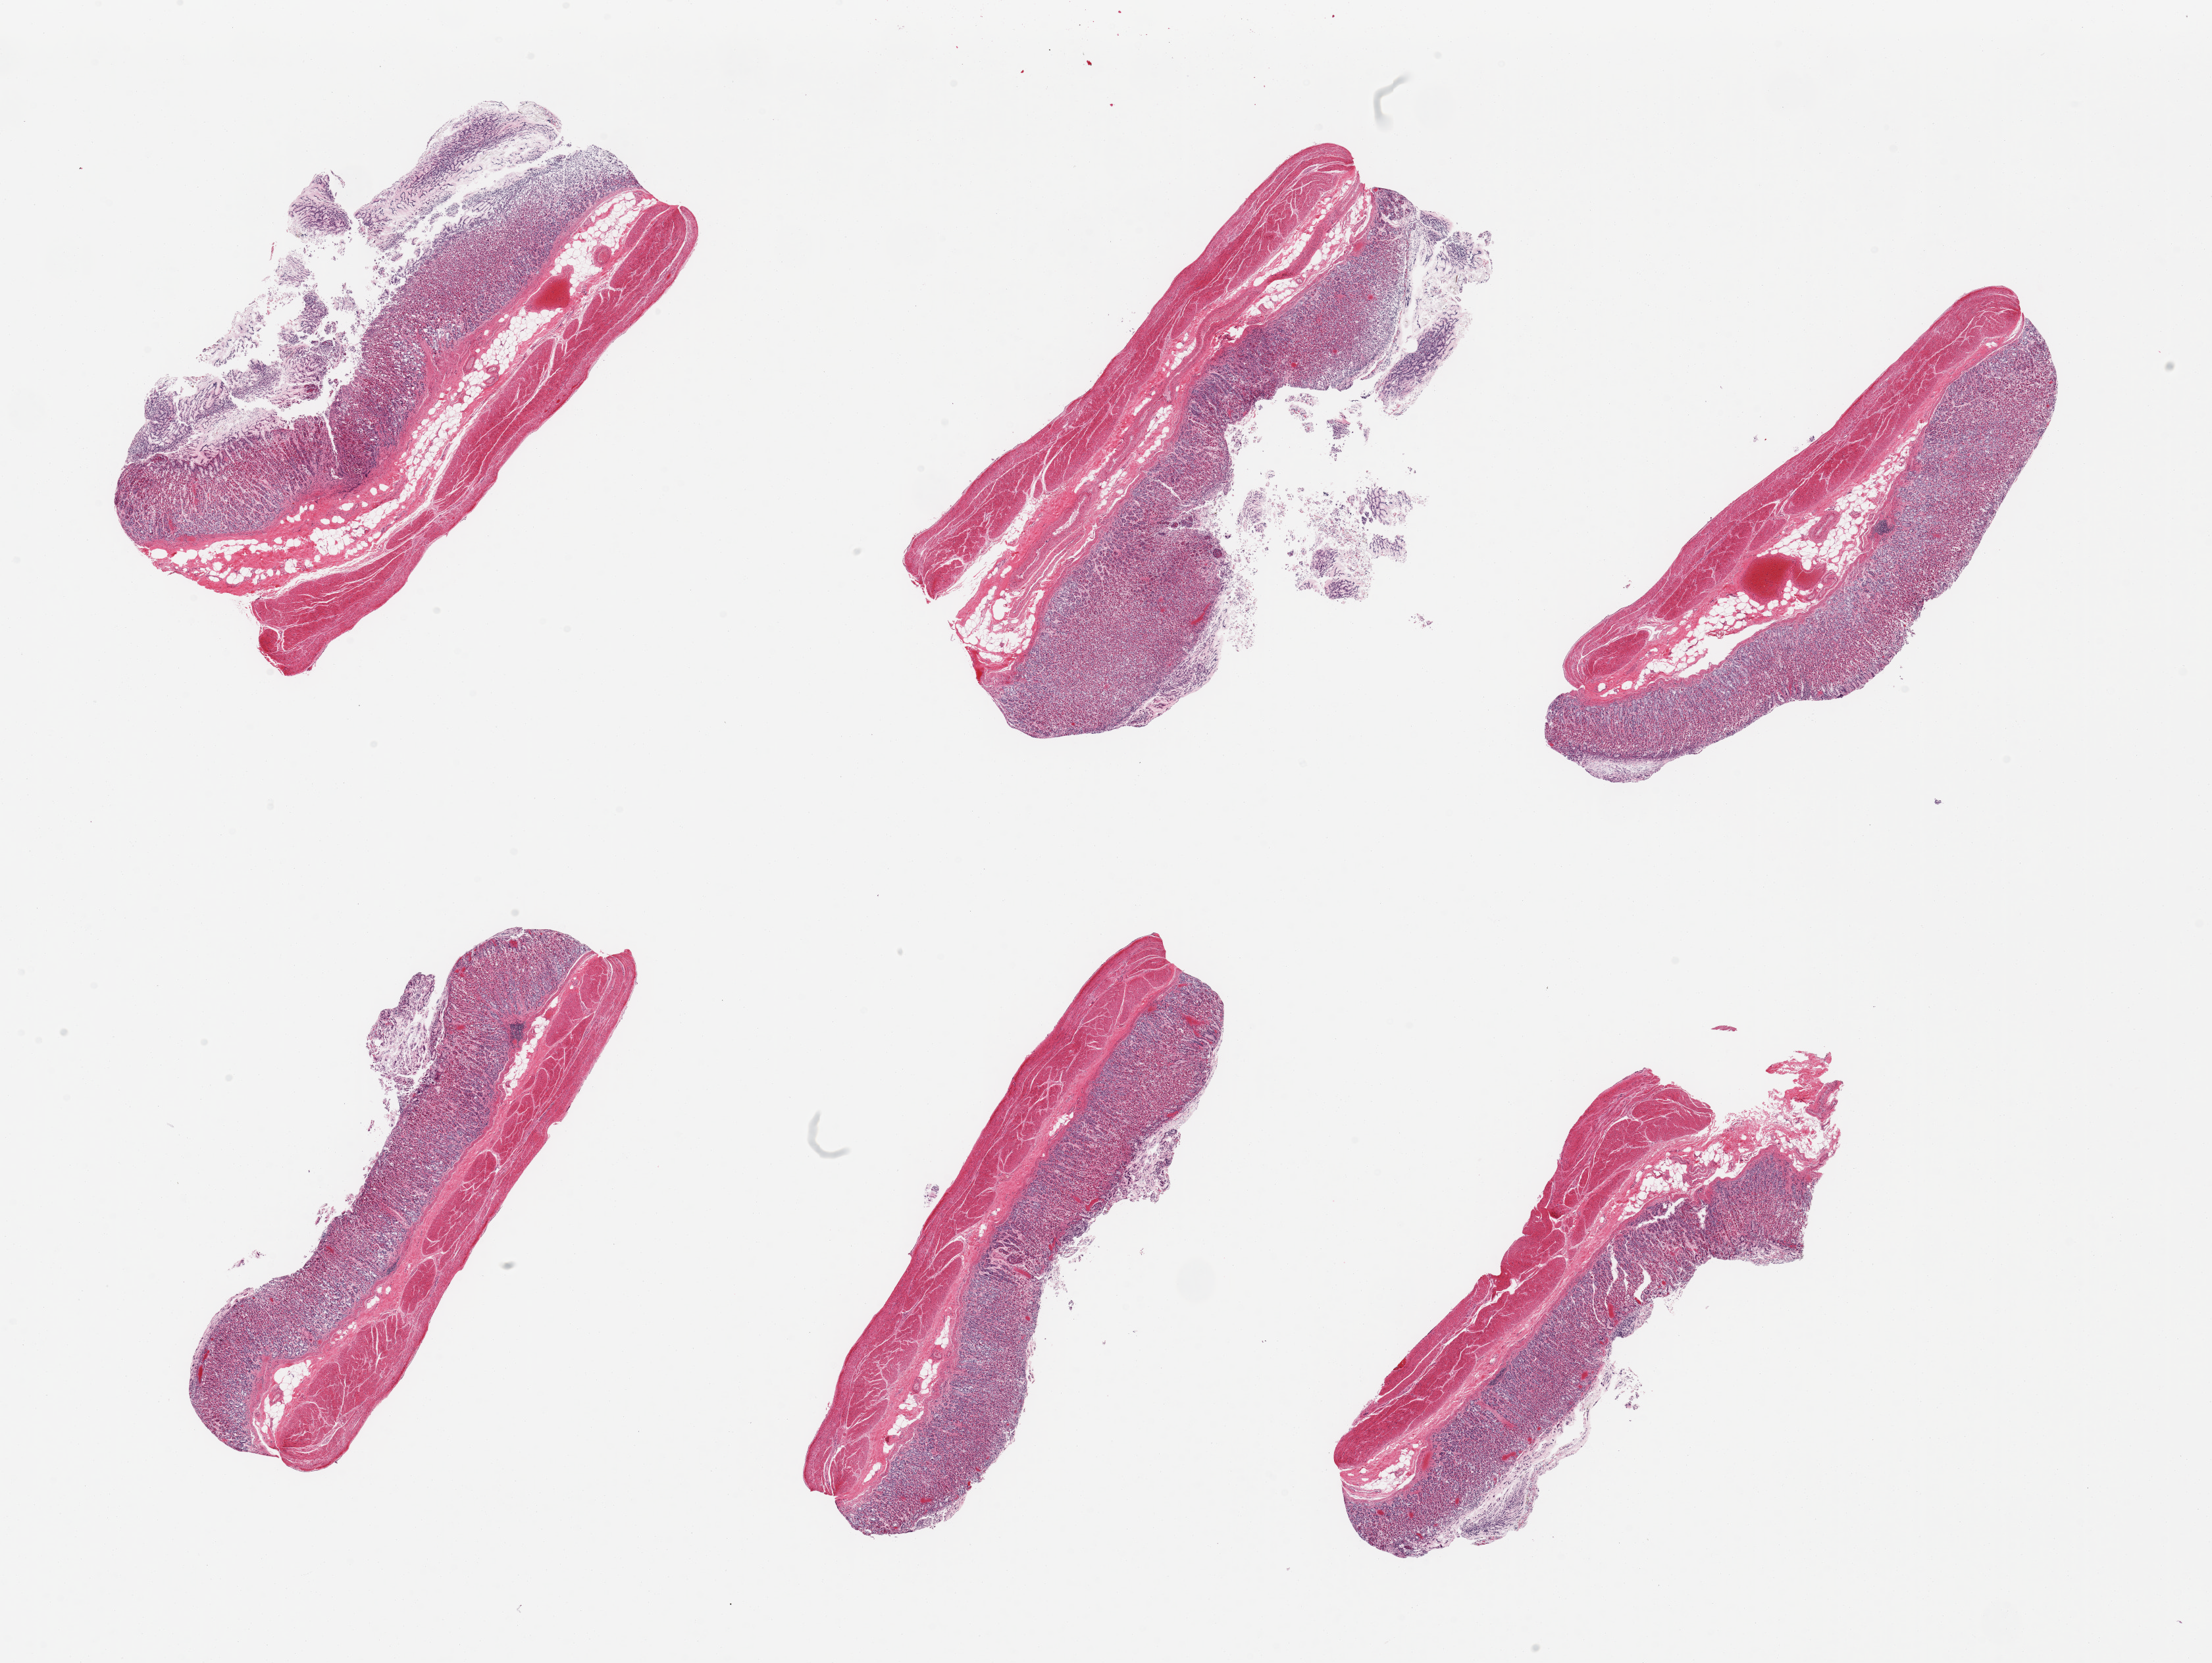
H&E whole-slide image — whole scanned area (about 26.6 x 20.0 mm, acquisition: 20x scan) shown as a low-resolution overview. PAXgene-fixed paraffin-embedded (PFPE) section. Section of stomach (target tissue). Tissue donor sample. Donor: male.
- reviewer comment on this tissue sample: 6 pieces, mucosa up to ~1mm, 40-60% of thickness